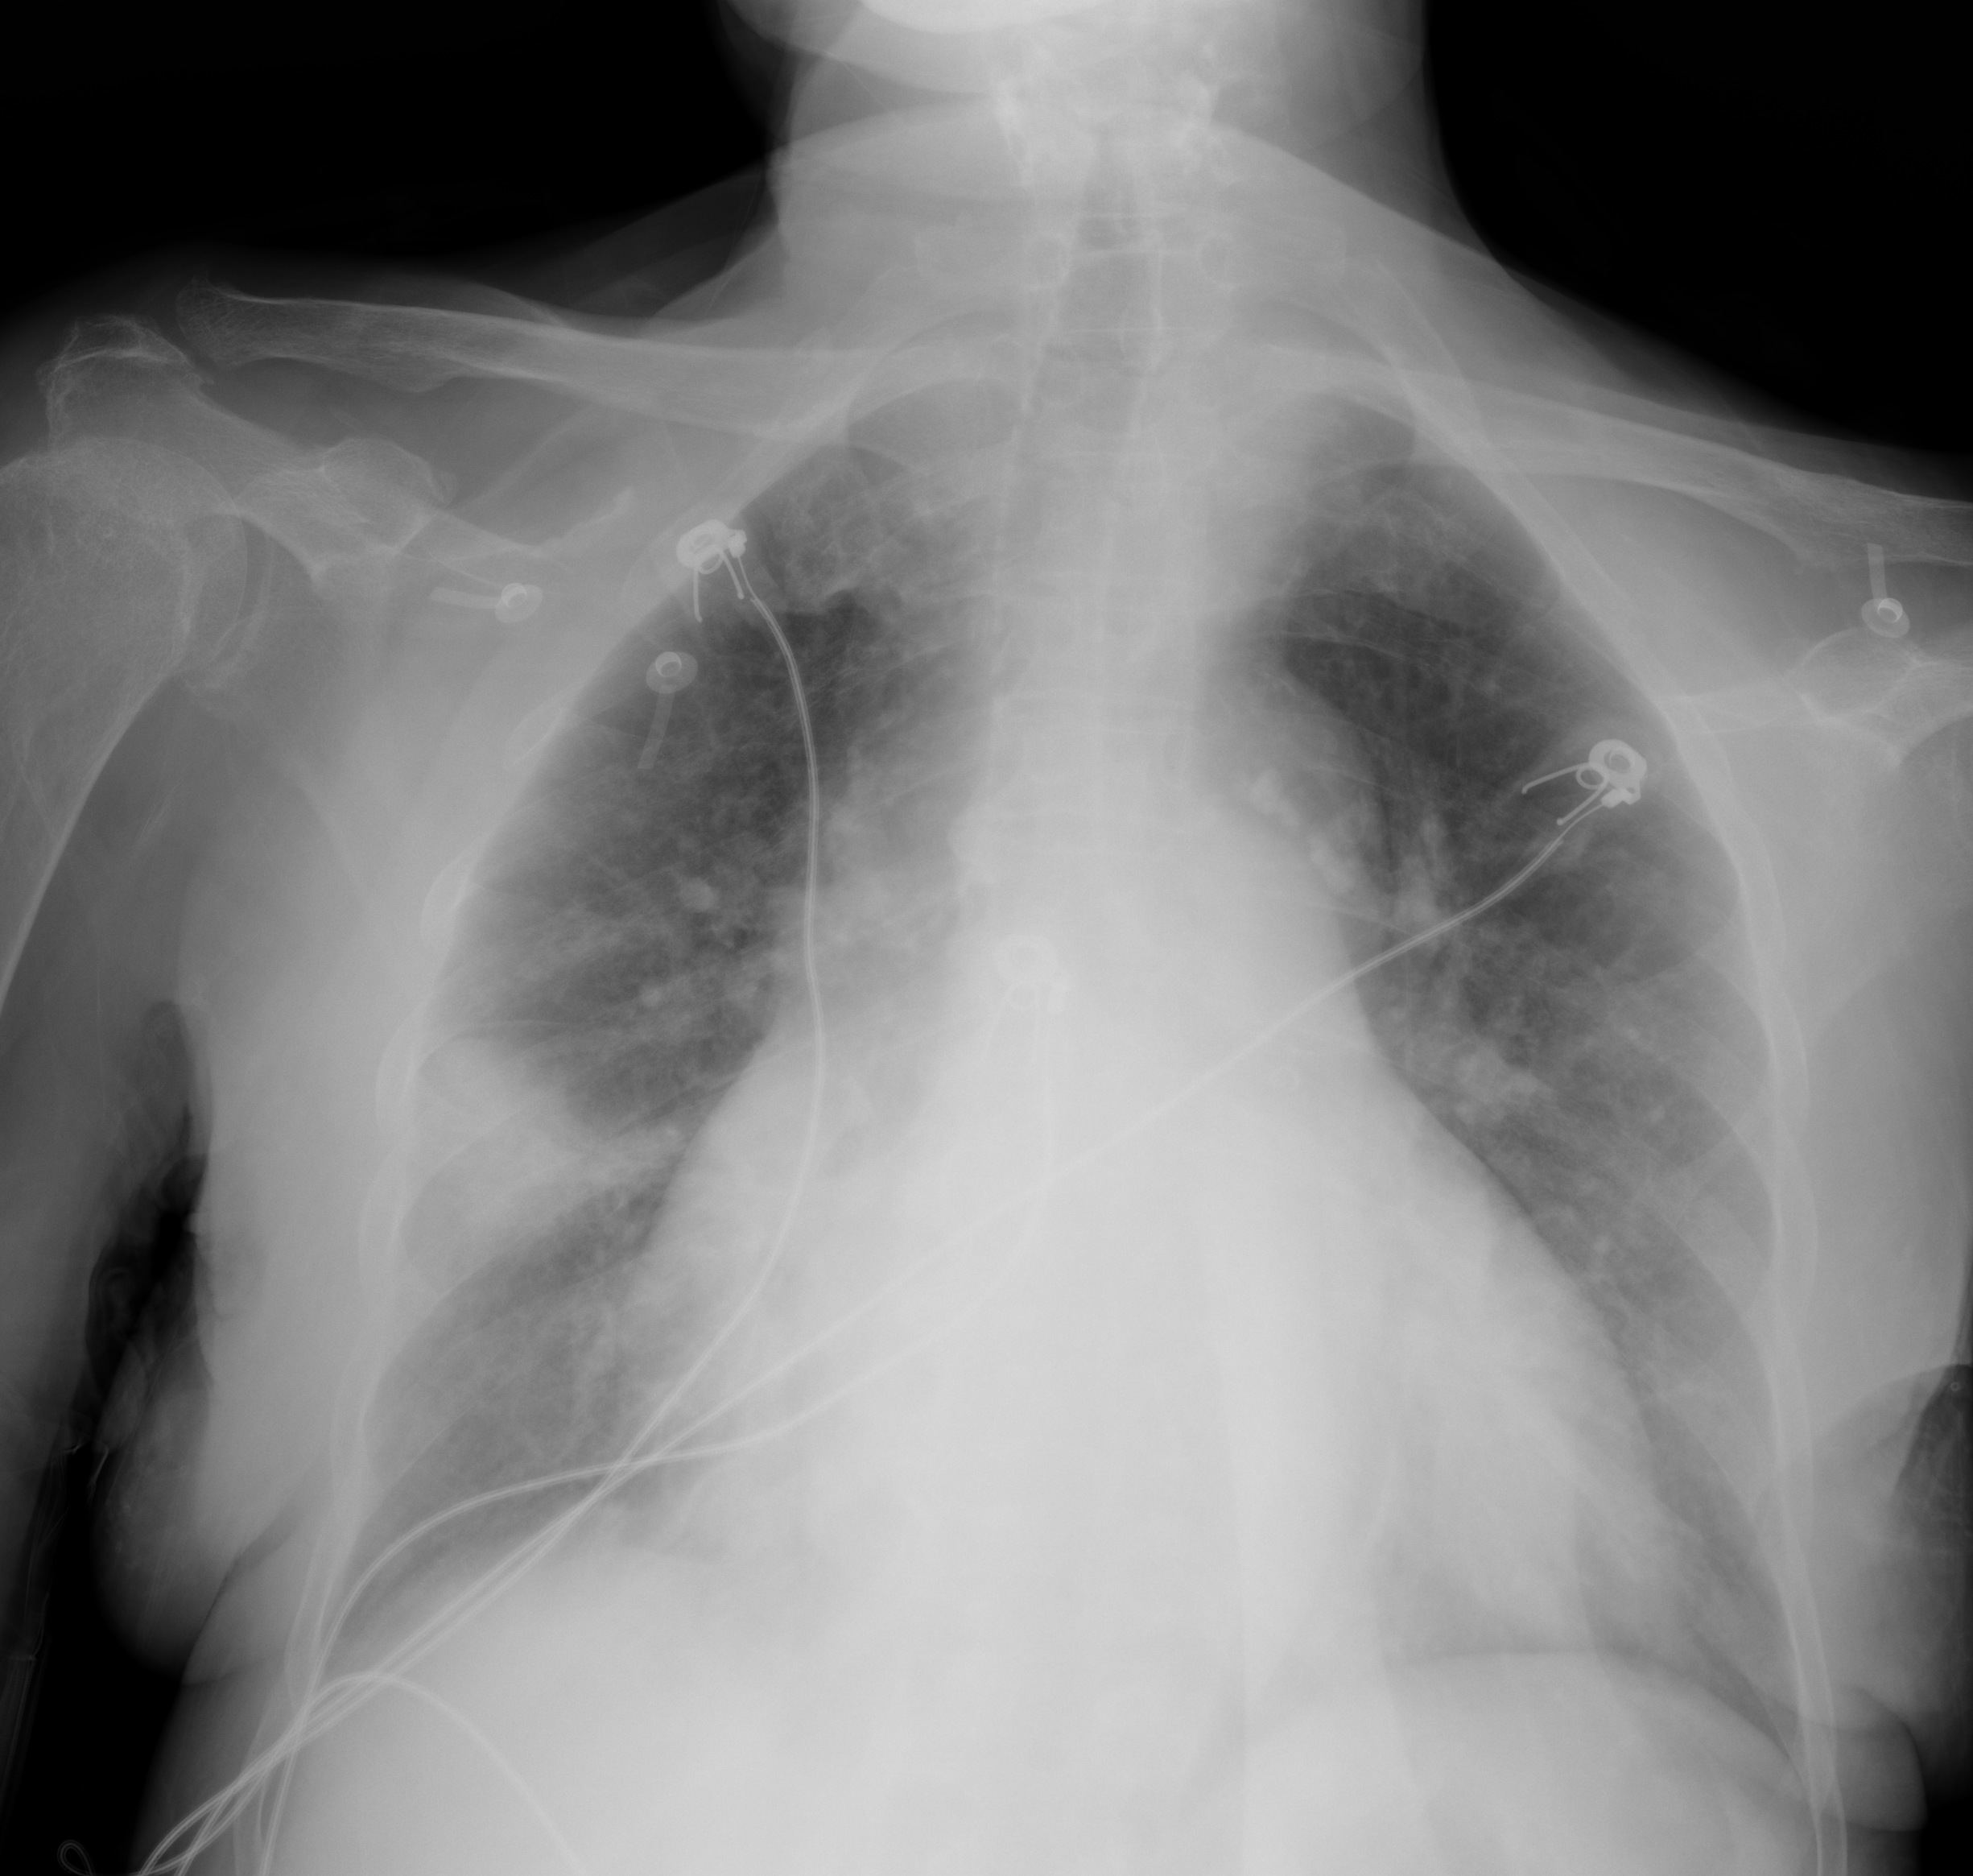
Chest X-ray (portable), AP projection. Female patient, age 74 years; imaged 0 days after the COVID-19 diagnosis.
Radiologist key findings (as recorded): Wedge shaped opacity in the right middle lobe.